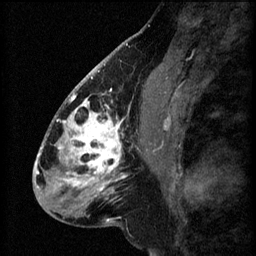
Breast MRI (dynamic contrast-enhanced), one sagittal slice. Position 29 of 60 along the scan axis. 3 images stored at this slice position (order not interpretable as contrast timing). 1.5 T. TE 4.2 ms, TR 8.2 ms. 2.2 mm slice thickness. 256 × 256 image matrix. Patient: female, 41 years.
Annotated regions visible in this slice (semi-automatically segmented with operator editing):
- analysis volume of interest (the breast-tissue region the enhancement analysis was run in; not a lesion): bounding box [x1, y1, x2, y2] px = [56, 104, 157, 207]
- tumour enhancement mask (voxels above the 70 % enhancement threshold inside the analysis volume of interest): [57, 104, 155, 197]